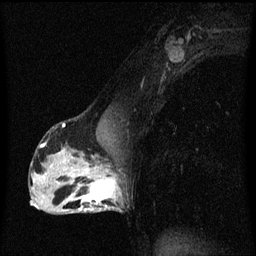
Breast MRI (dynamic contrast-enhanced), one sagittal slice; slice 34 of 60 in the series (ordered by position); dynamic contrast-enhanced series, image 2 of 3 at this slice position (ordered by acquisition); 1.5 T; TE 4.2 ms, TR 8.4 ms; 2 mm slice thickness; 256 × 256 image matrix, field of view 200 × 200 mm. Patient: female, 40 years.
Outlined on this slice (semi-automatic segmentation, software-assisted and operator-edited):
- analysis volume of interest (the breast-tissue region the enhancement analysis was run in; not a lesion): bounding box (x1, y1, x2, y2) in pixels: (76, 172, 123, 213)
- tumour enhancement mask (voxels above the 70 % enhancement threshold inside the analysis volume of interest): (76, 172, 122, 211)